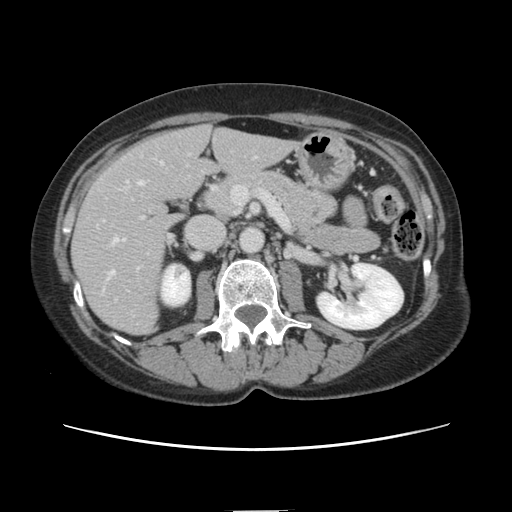
Contrast-enhanced abdominal CT, one axial slice; position 60 of 141 along the scan axis; 120 kVp; intravenous contrast given; soft-tissue window (W 400 / L 40 HU); 2.5 mm slice thickness; 512 × 512 image matrix, field of view 350 × 350 mm. Female patient, age 63 years. Case-level facts recorded for this patient, not image findings: diagnosis: colorectal cancer liver metastases, imaged before liver resection; multiple liver metastases: yes; largest metastasis: 3.2 cm; chemotherapy before resection: yes.
Outlined on this slice (manually delineated by an expert):
- hepatic veins: bounding box <108,181,143,278> (left, top, right, bottom; pixels)
- liver: <73,126,293,334>
- planned liver remnant (the part of the liver to remain after resection): <177,126,293,188>
- portal vein (with intrahepatic branches): <119,180,131,241>